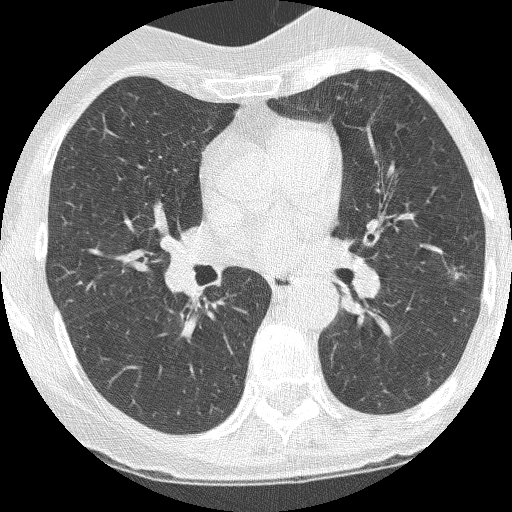
Chest CT (low-dose screening protocol), one axial image. Third screening round (two years after baseline). Lung window (W 1500 / L -600 HU). Lung (sharp) reconstruction kernel (BONE). 512 × 512 image matrix. Female participant, aged 60 years at enrolment. Current smoker at enrolment.
Expert reader's lesion annotation, bounding box (x1, y1, x2, y2) in pixels: (435, 260, 472, 291). The screening reader recorded 2 non-calcified nodules or masses ≥4 mm on this exam (left upper lobe, left upper lobe); which of them this box marks is not recorded. Official screen result: positive, other. Participant outcome: lung cancer diagnosed 37 days after this screen — adenocarcinoma, NOS, left upper lobe, moderately differentiated (G2), stage IA (AJCC 6th edition), 6 mm at pathology.